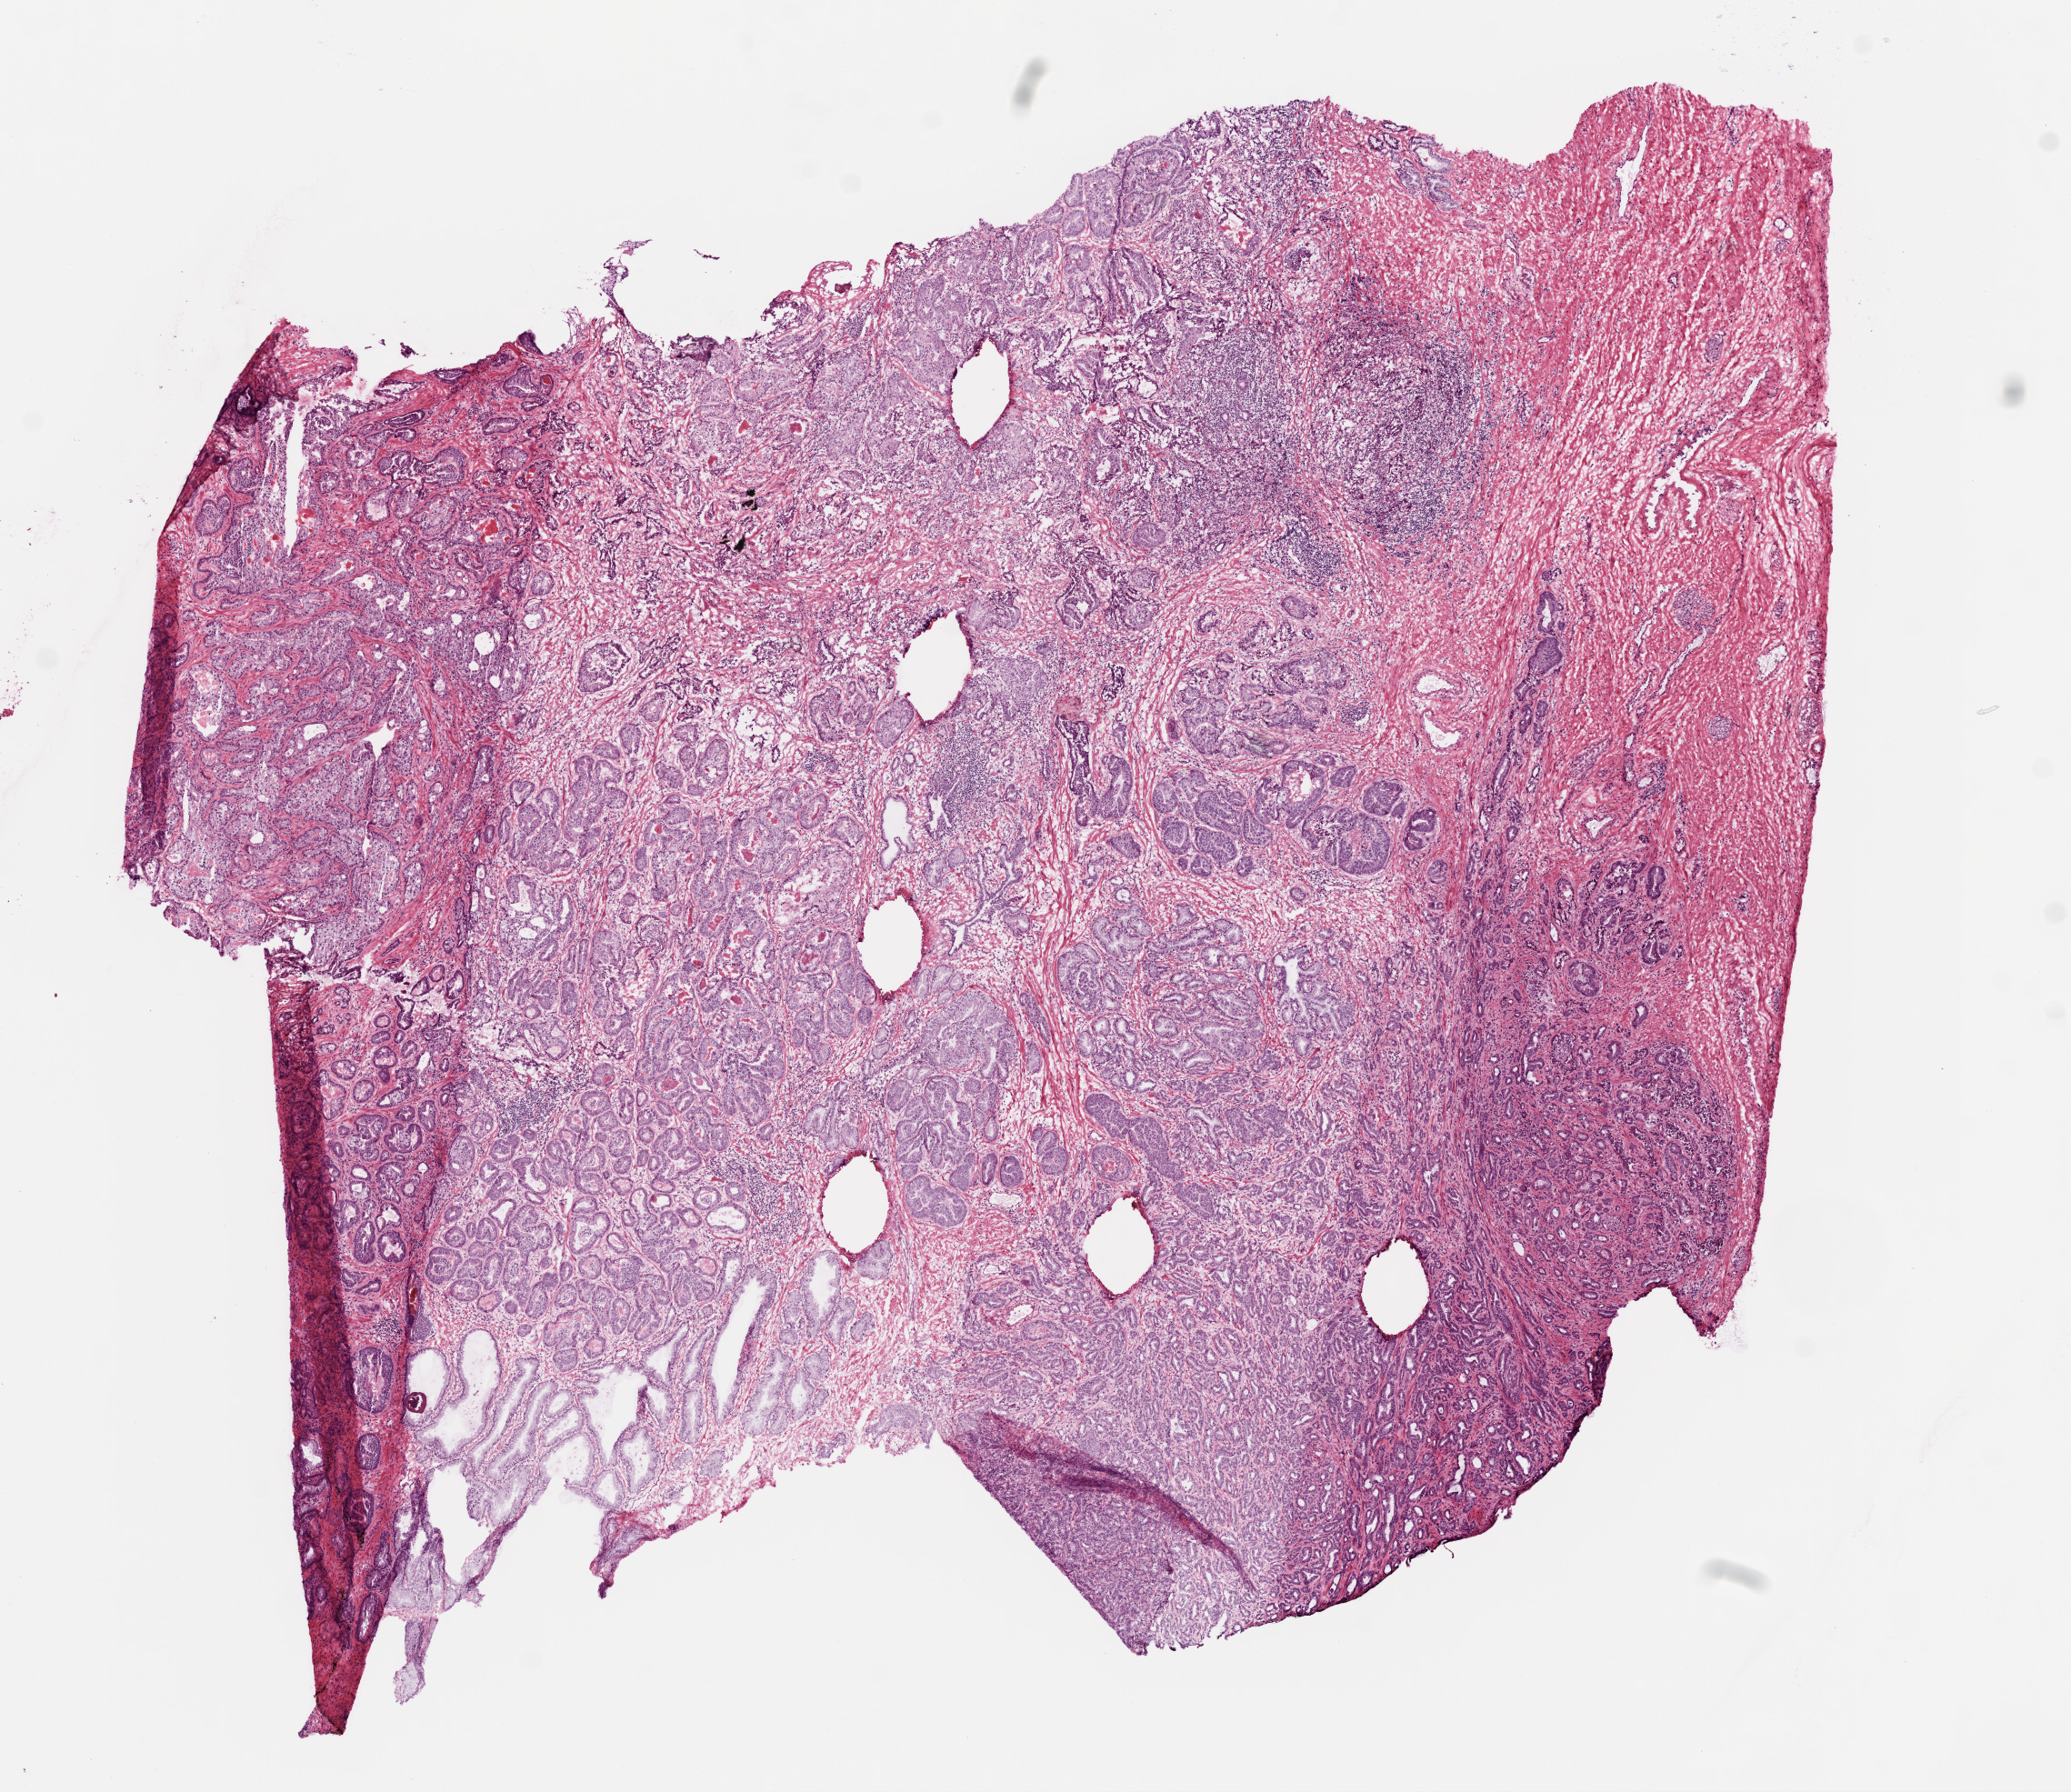
Digitized H&E tissue section (whole slide), whole scanned area (about 9.2 x 7.9 mm) shown as a low-resolution overview. Frozen section from the top of the tissue portion. Sample: primary tumour, prostate. Male, age 66 years at initial diagnosis.
Pathologic diagnosis: Acinar cell carcinoma (prostate gland).